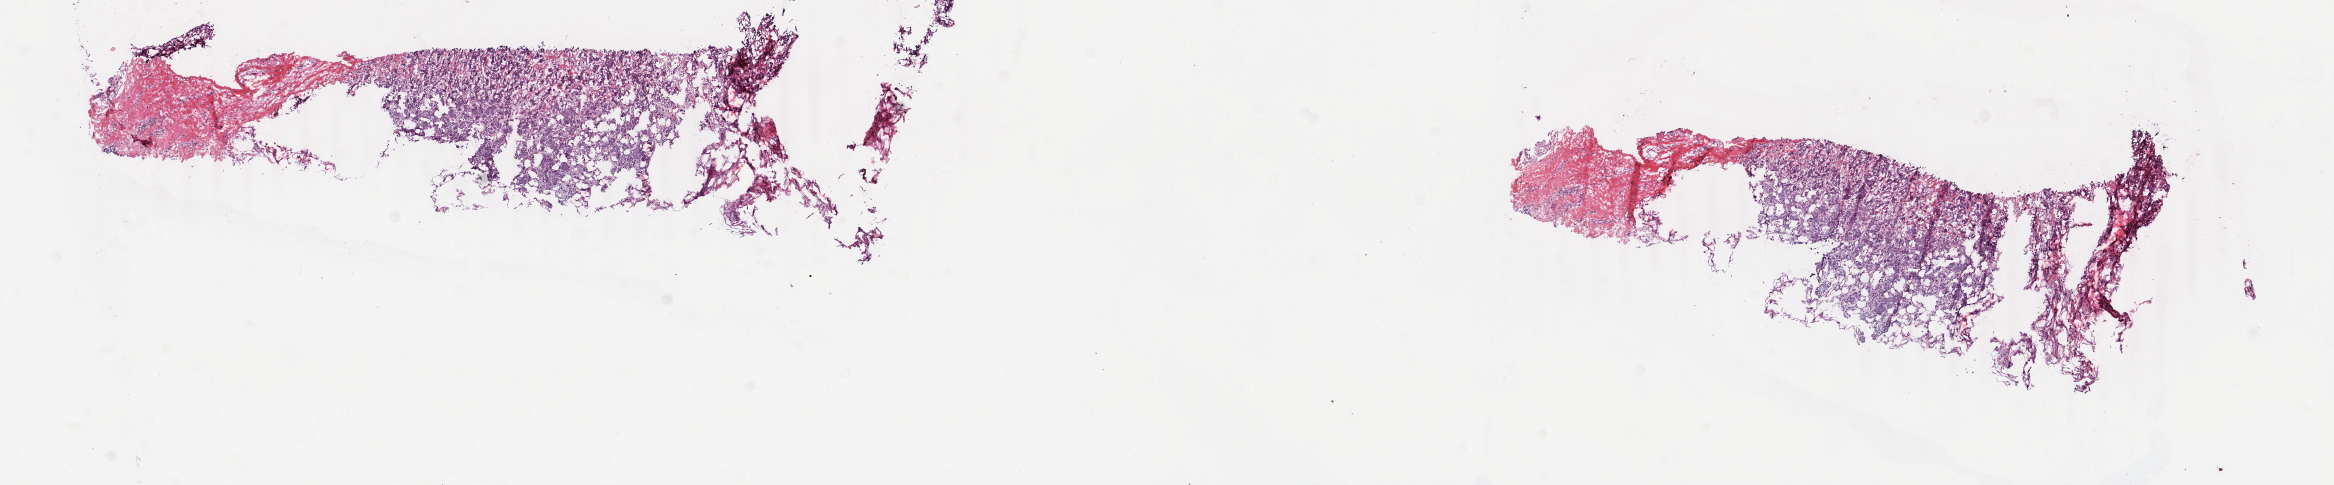
Digitized H&E-stained tissue section (whole slide) — low-resolution overview of the scanned area, about 18.6 x 3.9 mm, frozen section, primary tumour sample from the breast. Patient: female, age at initial diagnosis 62 years. Composition of this section per pathologist review: tumour cells 80%, tumour nuclei 85%, normal cells 0%, stromal cells 18%, necrosis 2%. Infiltration values recorded for this section: lymphocyte infiltration 4%, monocyte infiltration 2%, neutrophil infiltration 0%.
- AJCC pathologic stage: IIA
- pathologic diagnosis: Infiltrating duct carcinoma, NOS
- laterality: left
- TNM: T2 N0 M0